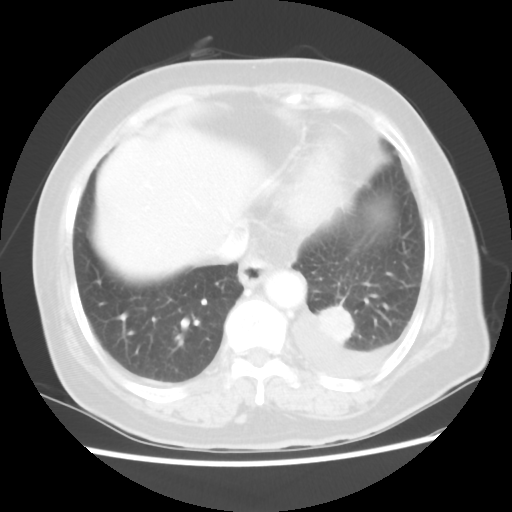
Chest CT, one axial slice; position 14 of 80 along the scan axis; lung window (W 1500 / L -600 HU); 5 mm slice thickness; 512 × 512 image matrix. Female patient, age 68 years. Case-level facts recorded for this patient, not image findings: clinical TNM (as recorded): T1c N0 M1.
Annotated regions visible in this slice (rectangle marked by the reading radiologist):
- lung tumour (recorded histology: adenocarcinoma): bounding box <315,303,362,346> (left, top, right, bottom; pixels)